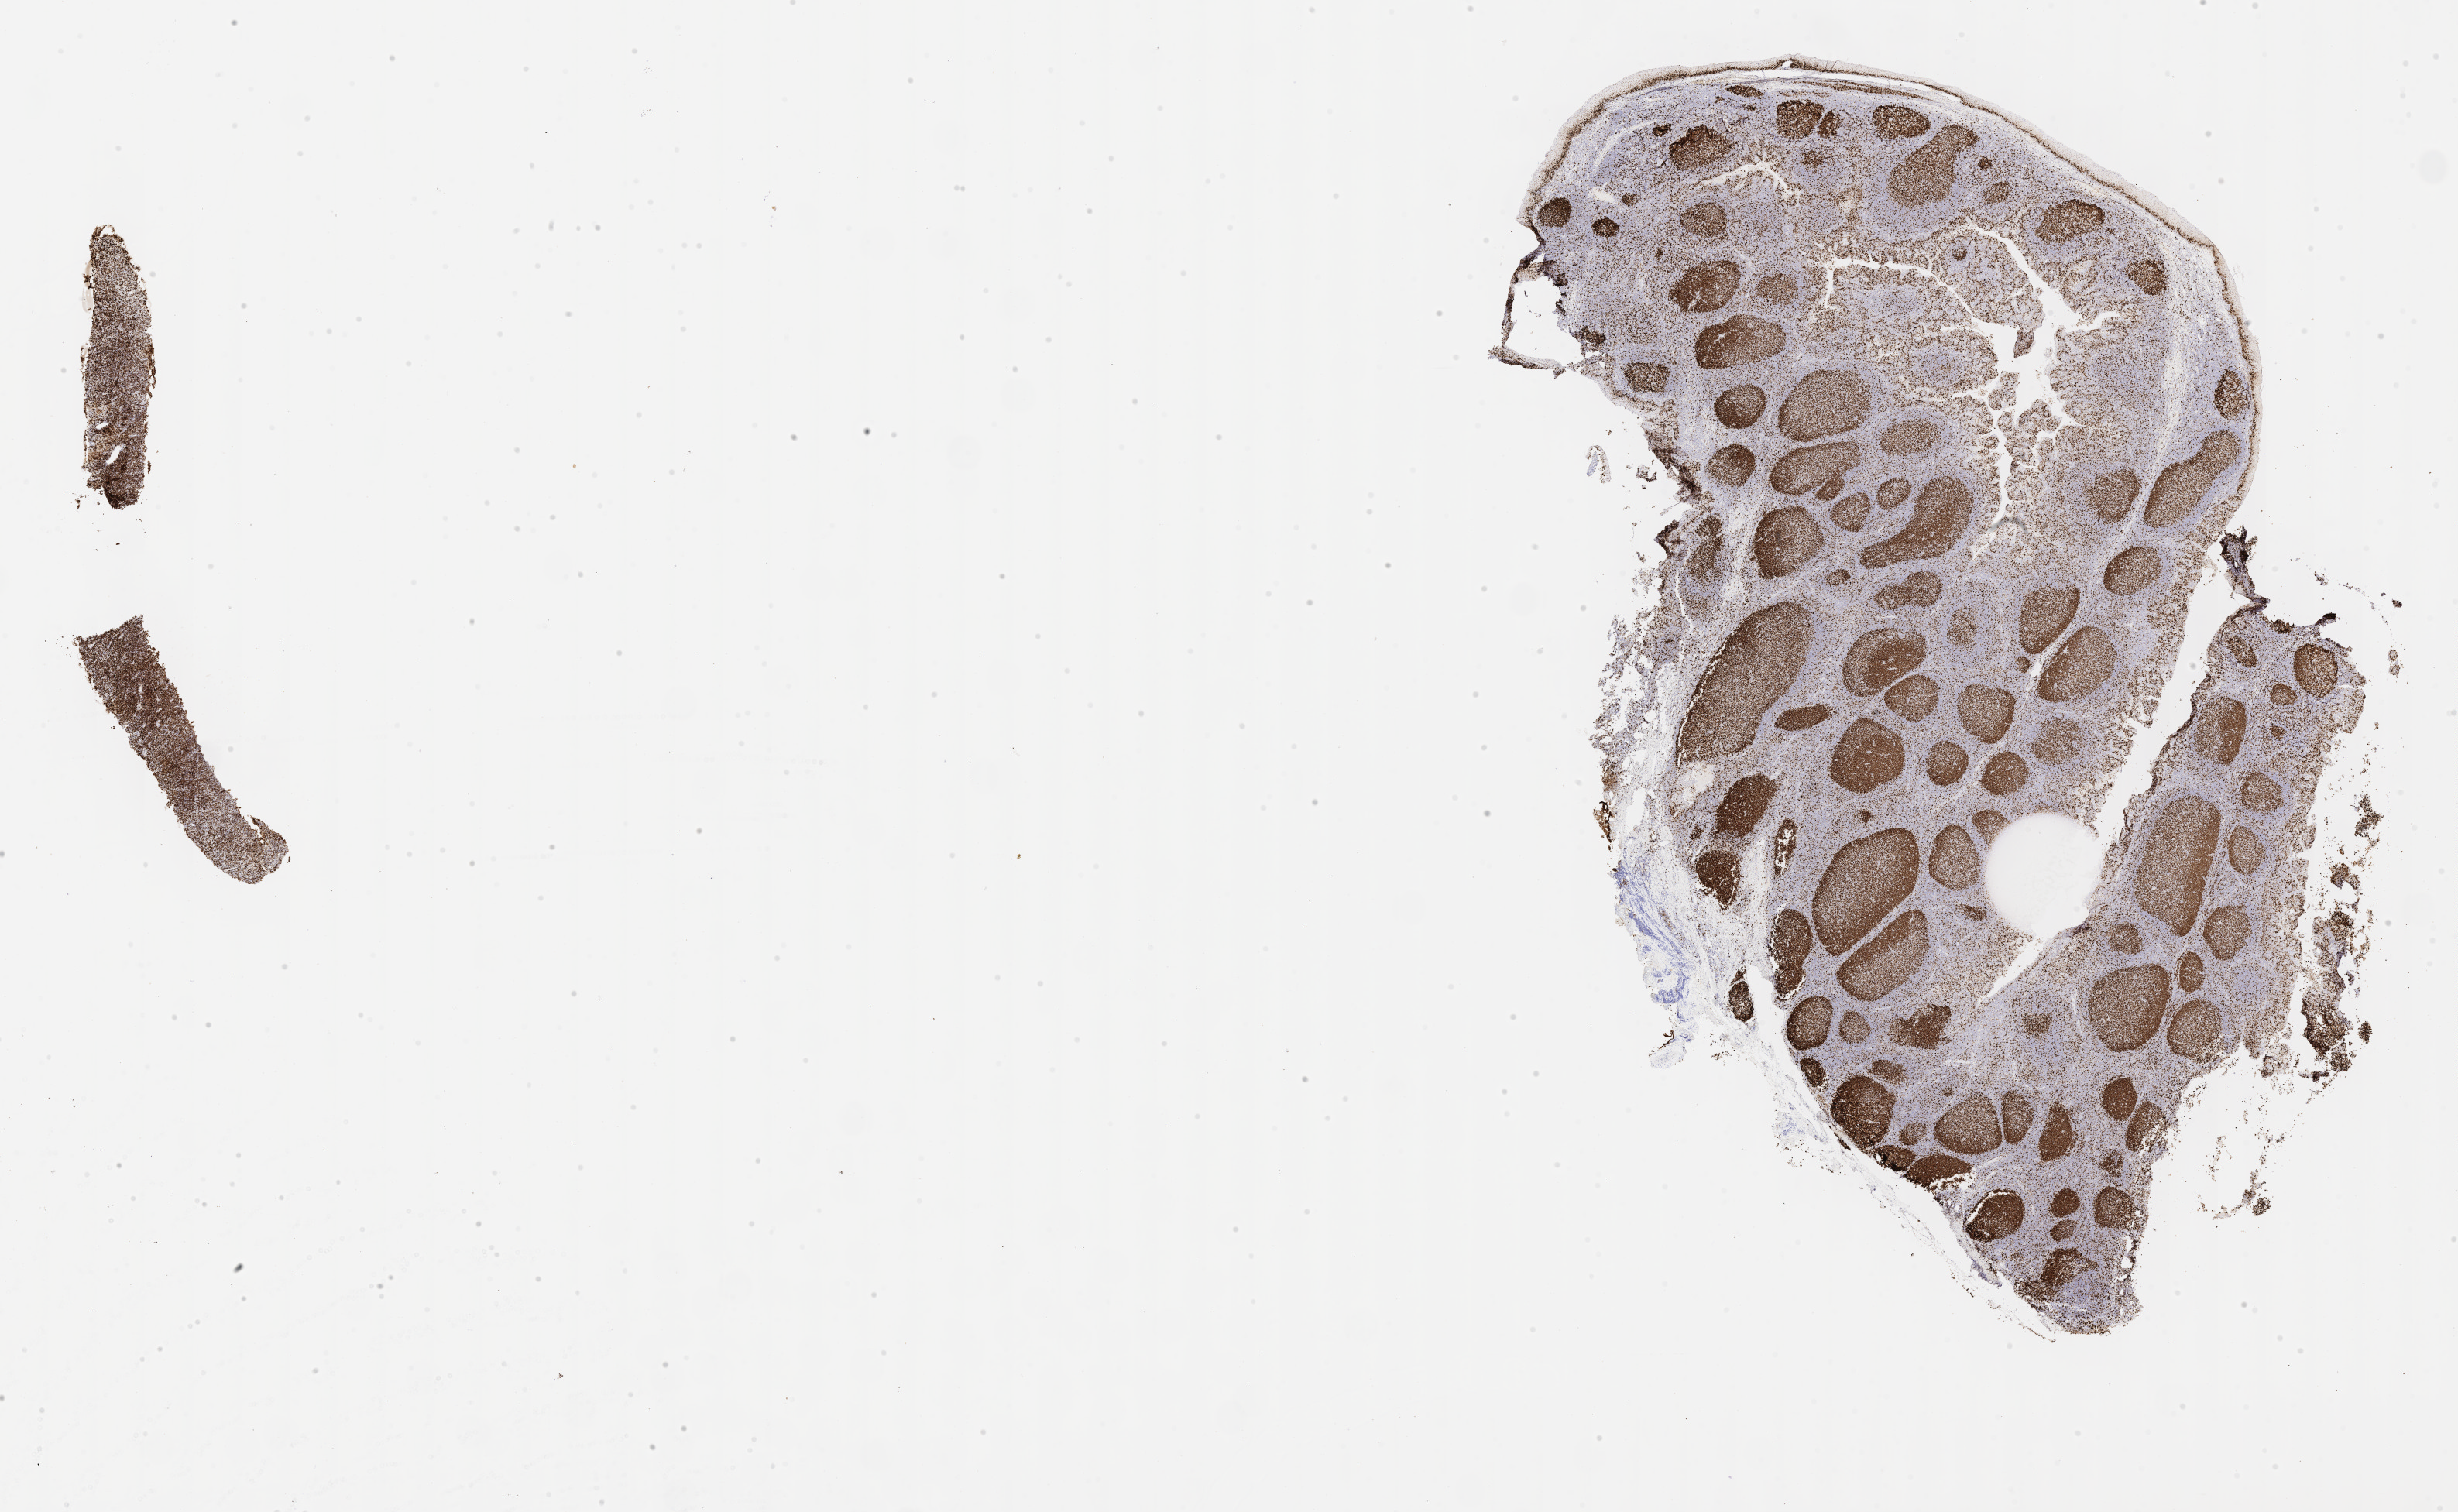
Whole-slide image, immunohistochemical stain for Ki-67 — shown as a low-resolution overview of the whole scanned area (about 25.7 x 15.8 mm). Patient sex: male.
* specimen: tumor tissue